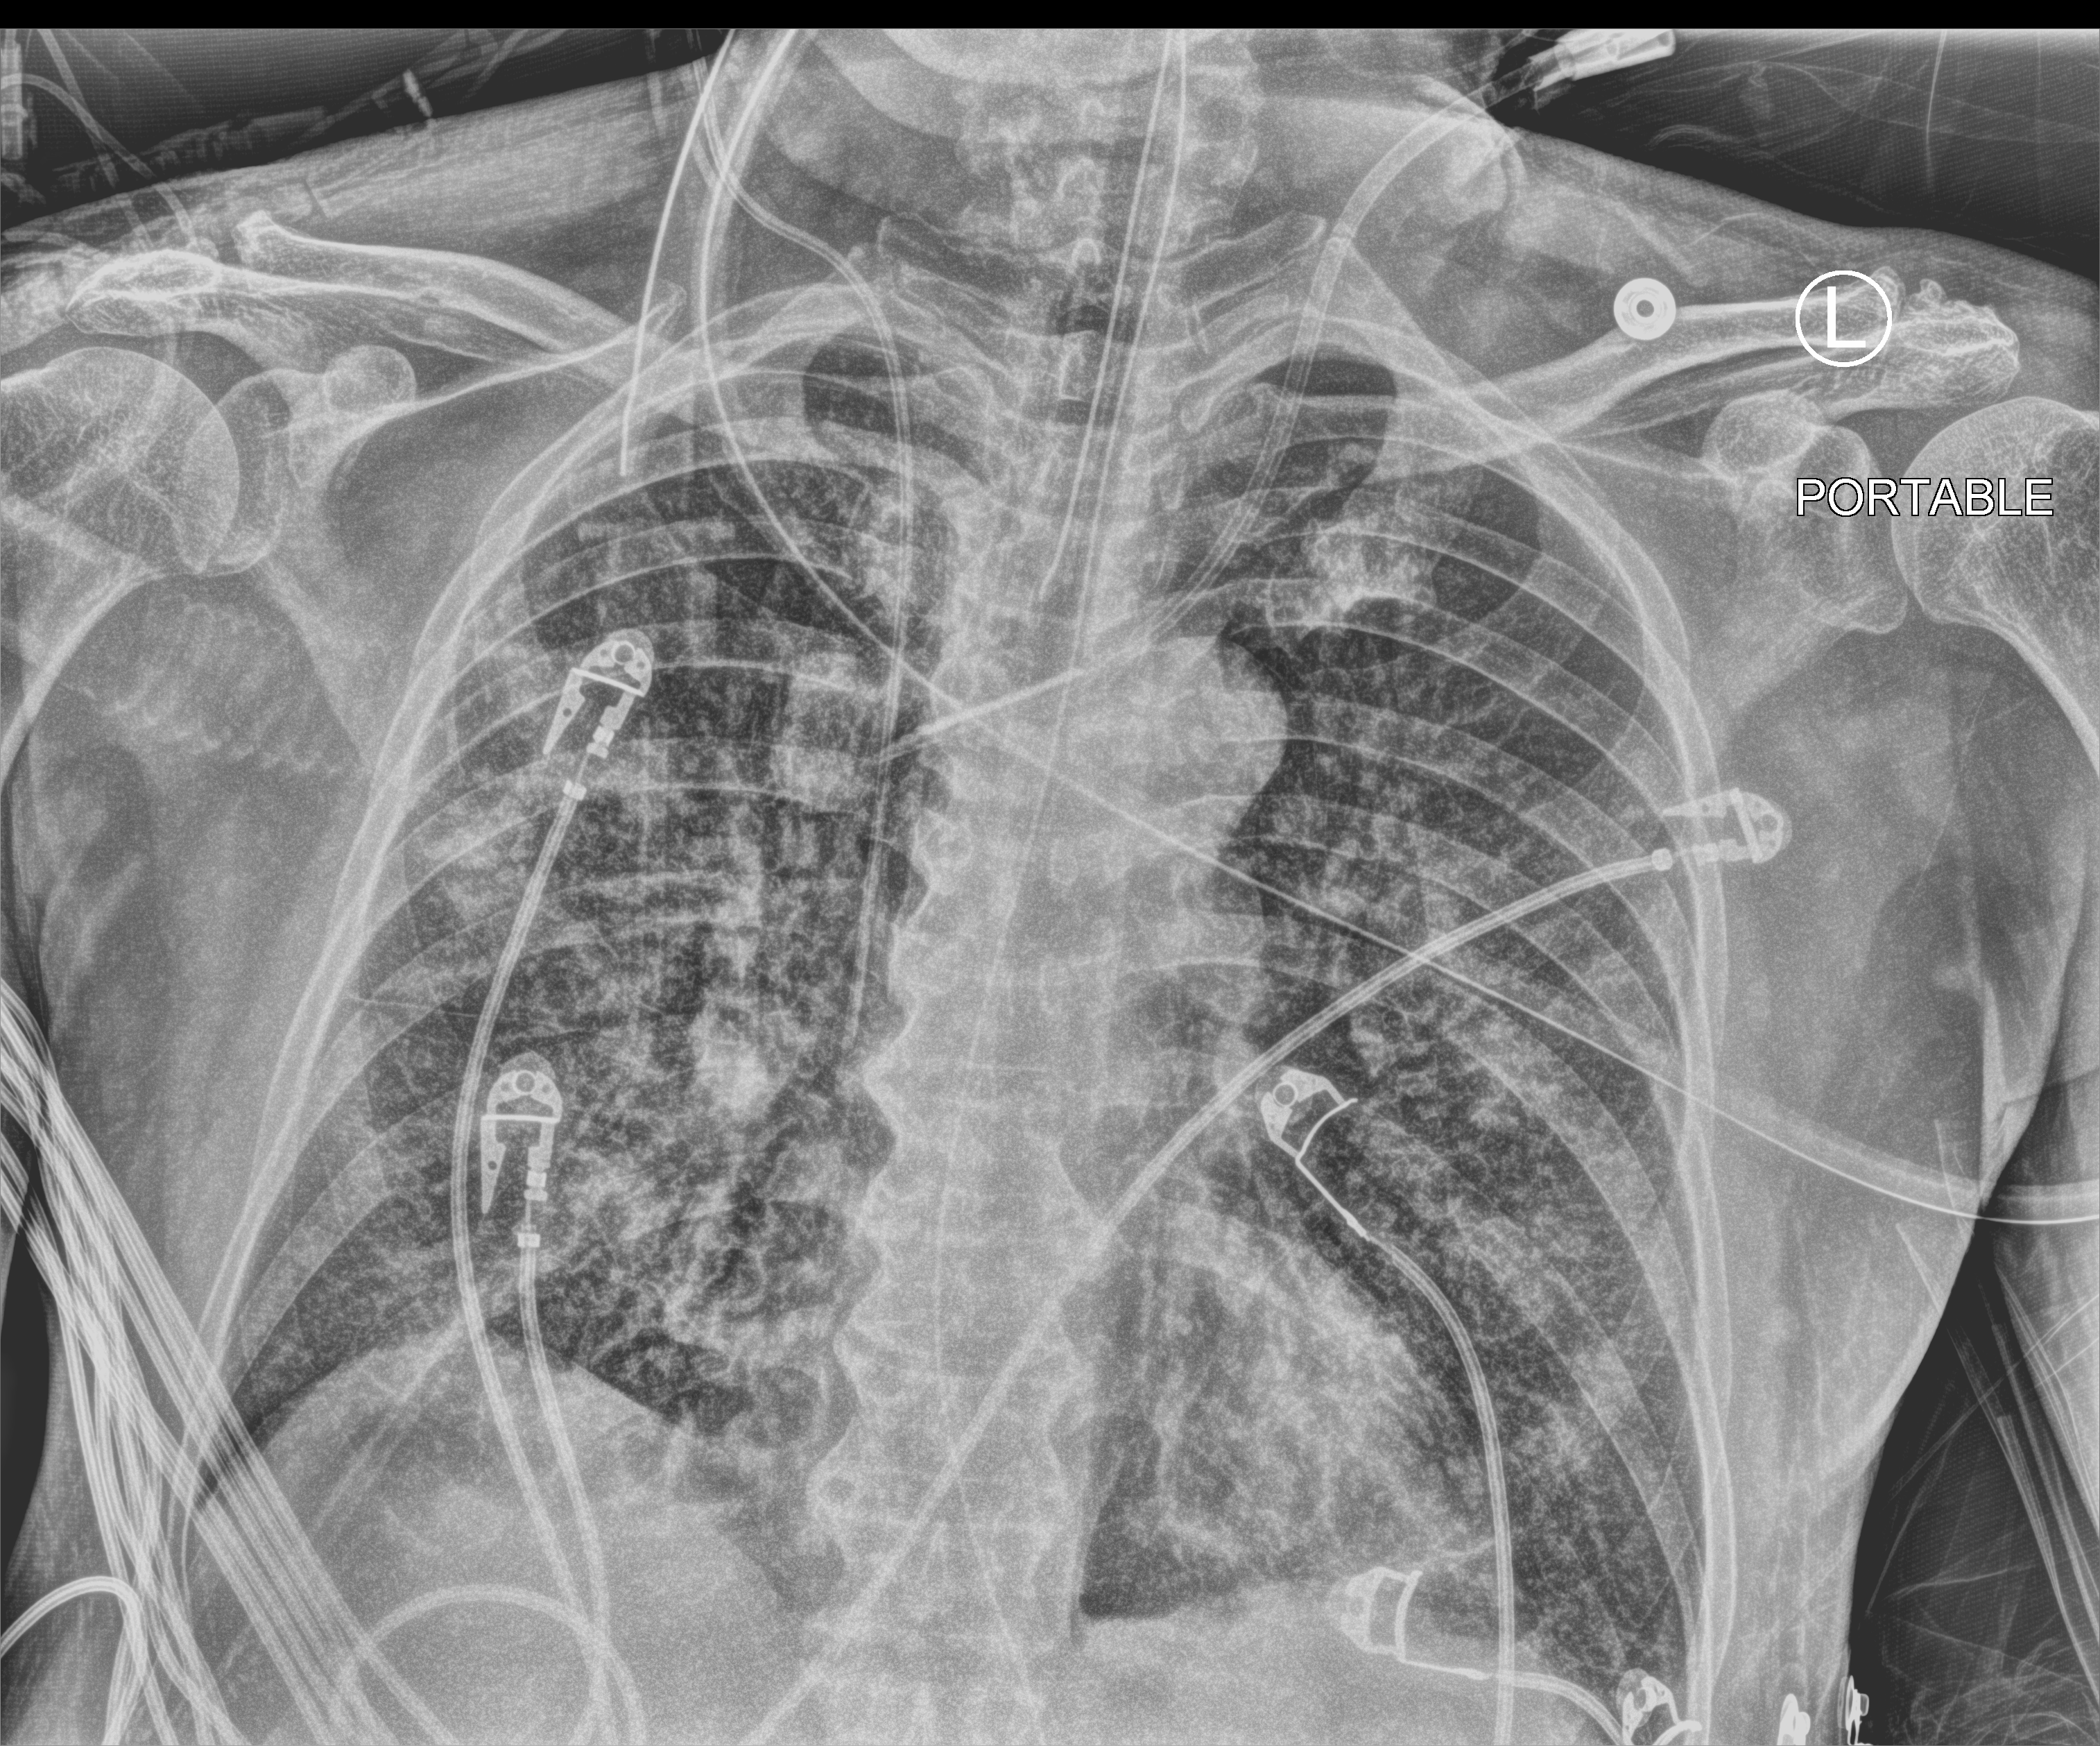
Chest X-ray (portable), anteroposterior (AP) projection. Patient hospitalised with COVID-19; male, aged 60–74 years.
Hospital-stay facts (about this admission, not read from this image; timing relative to this image not recorded): hypertension (admission record): yes; mechanically ventilated during this hospital stay: yes.